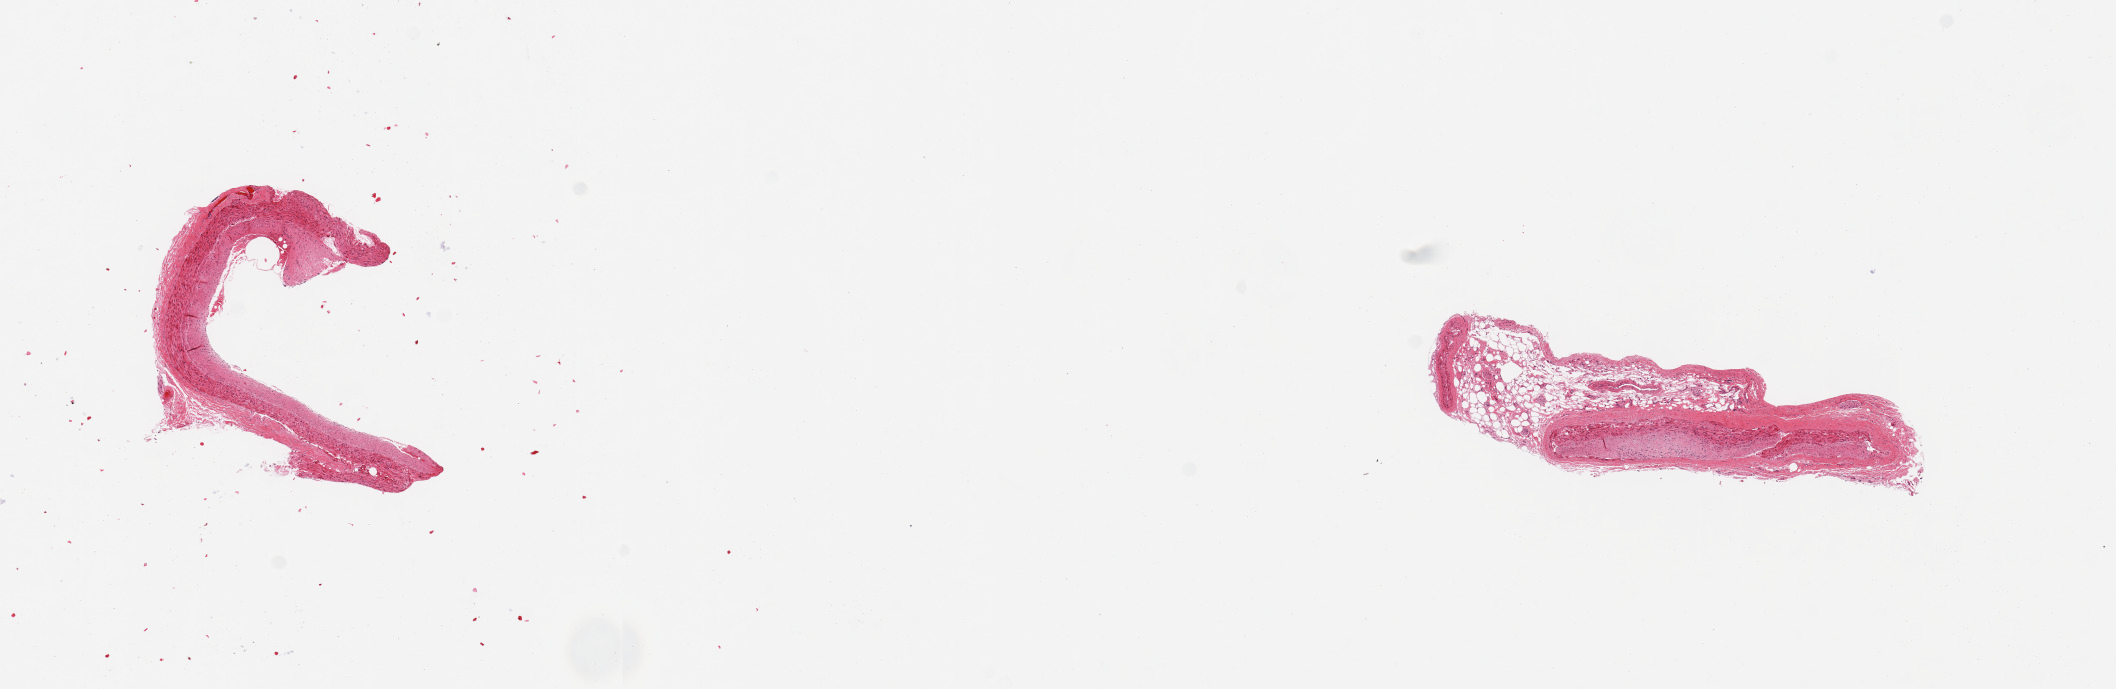
Whole-slide image, haematoxylin and eosin stain — whole scanned area (about 16.7 x 5.4 mm, from a 20x scan) shown as a low-resolution overview, PAXgene-fixed, paraffin-embedded tissue, section of coronary artery (target tissue), donor tissue sample. Male donor.
Reviewer comment on this tissue sample: 2 pieces; fragment of artery wall and cross section of vessel with collapsed lumen, 30%attached fat.